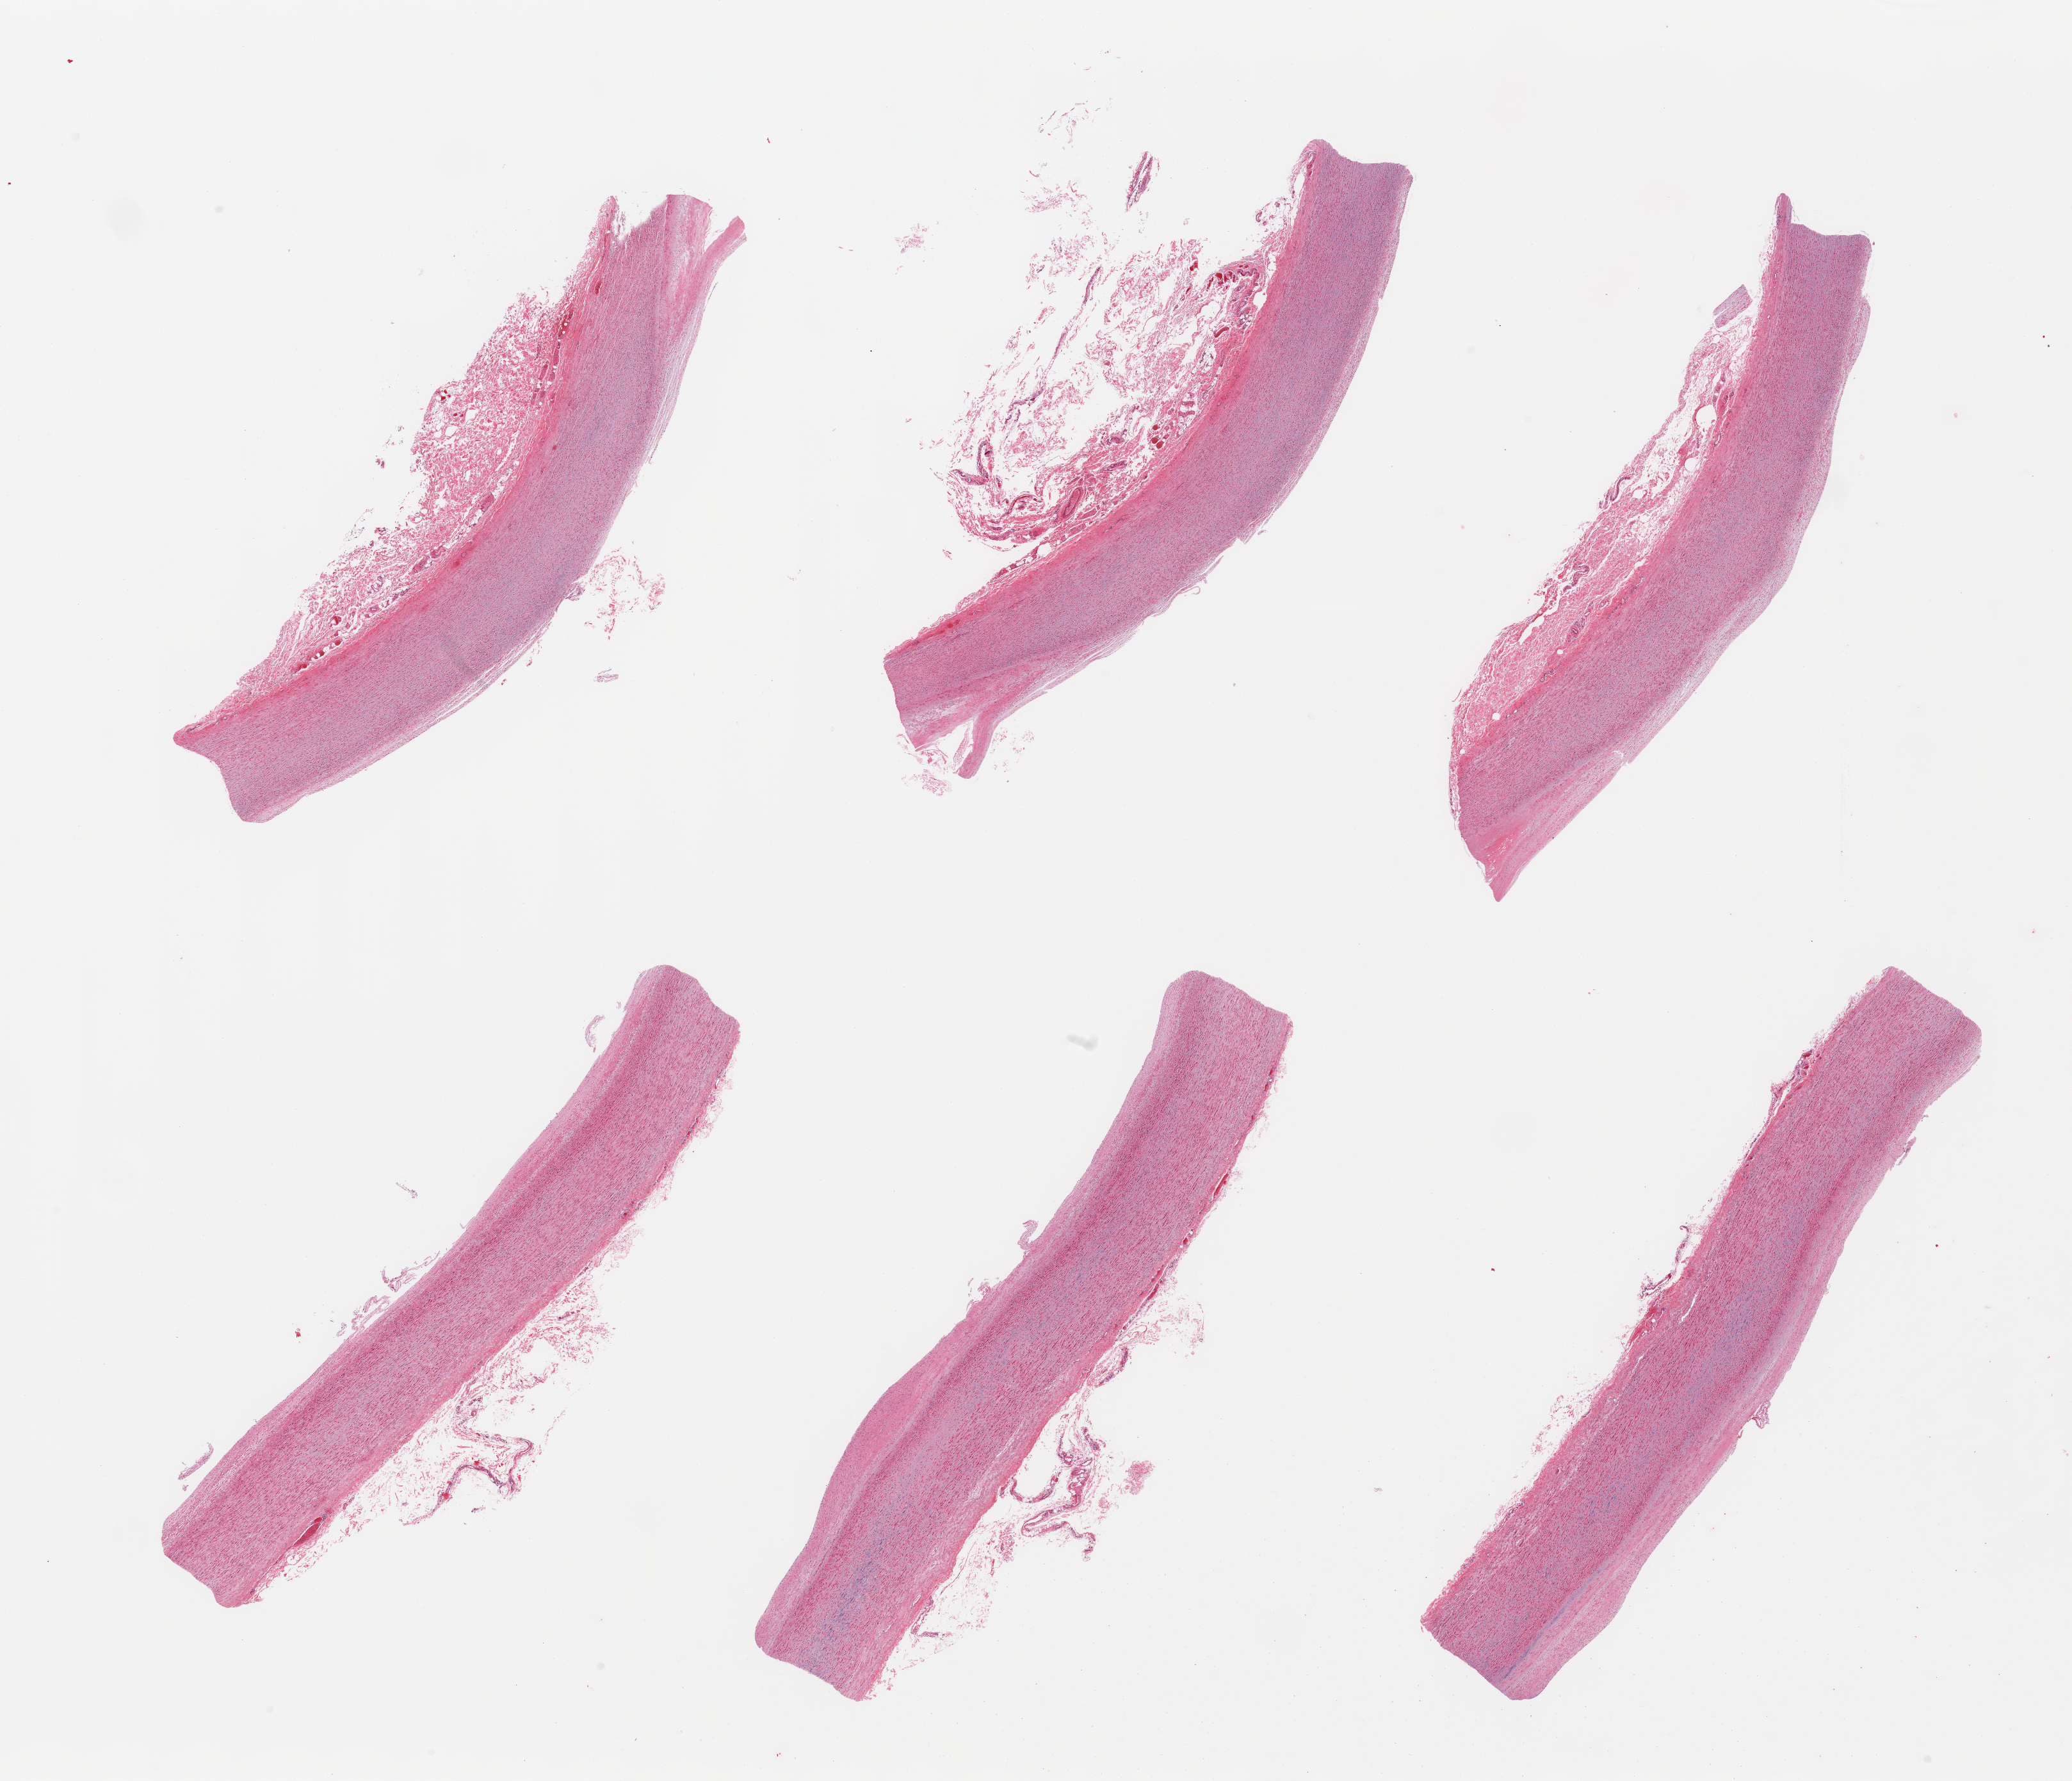
Whole-slide image, H&E stain, a low-resolution overview of the entire scanned area, about 25.6 x 22.0 mm (acquisition: 20x scan), PAXgene-fixed paraffin-embedded (PFPE) section, sampled site (target tissue): aorta, donor tissue sample. Donor: female.
Pathologist's review note for this sample: 6 pieces, atherosis up to ~0.5mm; nubbins of adherent serosa up to ~2mm.